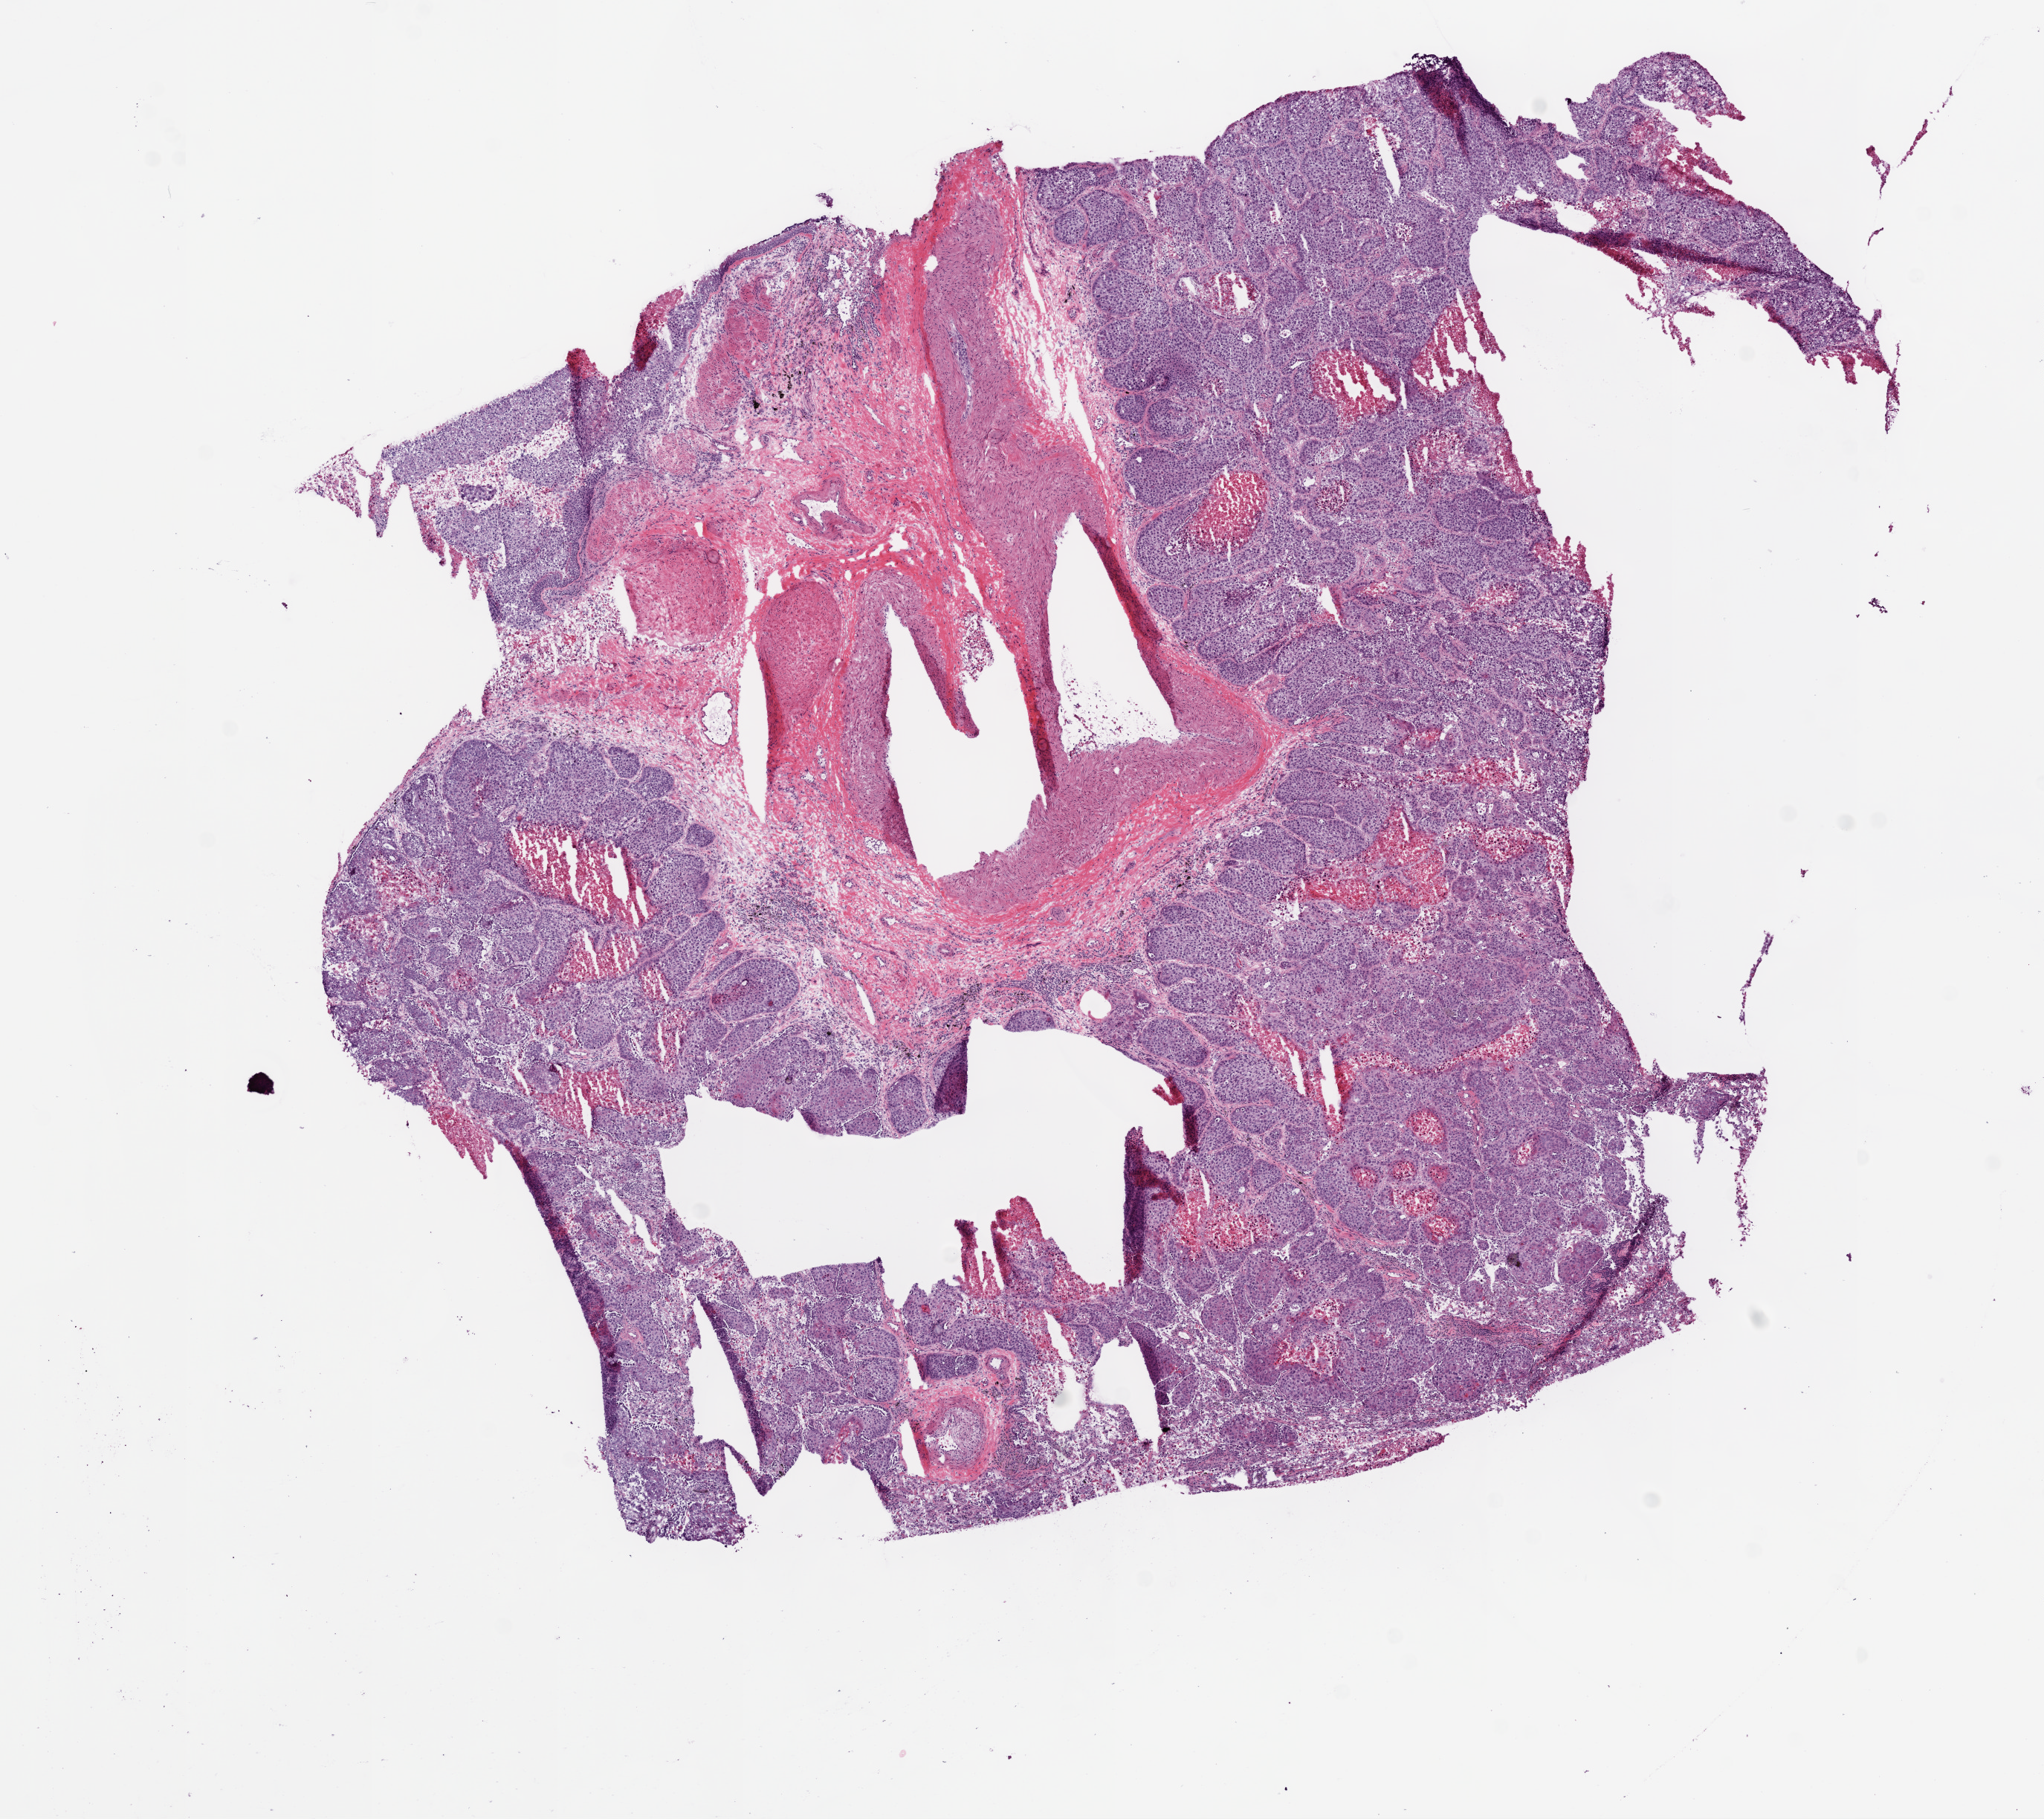
Hematoxylin and eosin (H&E) stained whole-slide image — a low-resolution overview of the entire scanned area, about 11.0 x 9.8 mm (slide scanned at 20x), frozen section from the bottom of the tissue portion, primary tumour sample from the lung. Patient: male, age at initial diagnosis 52 years. Composition of this section per pathologist review: tumour cells 65%, tumour nuclei 75%, normal cells 20%, necrosis 15%. Infiltration values recorded for this section: lymphocyte infiltration 5%.
• AJCC pathologic stage: IB (6th edition)
• laterality: left
• TNM: T2a N0 M0
• pathologic diagnosis: Squamous cell carcinoma, NOS (lower lobe, lung)